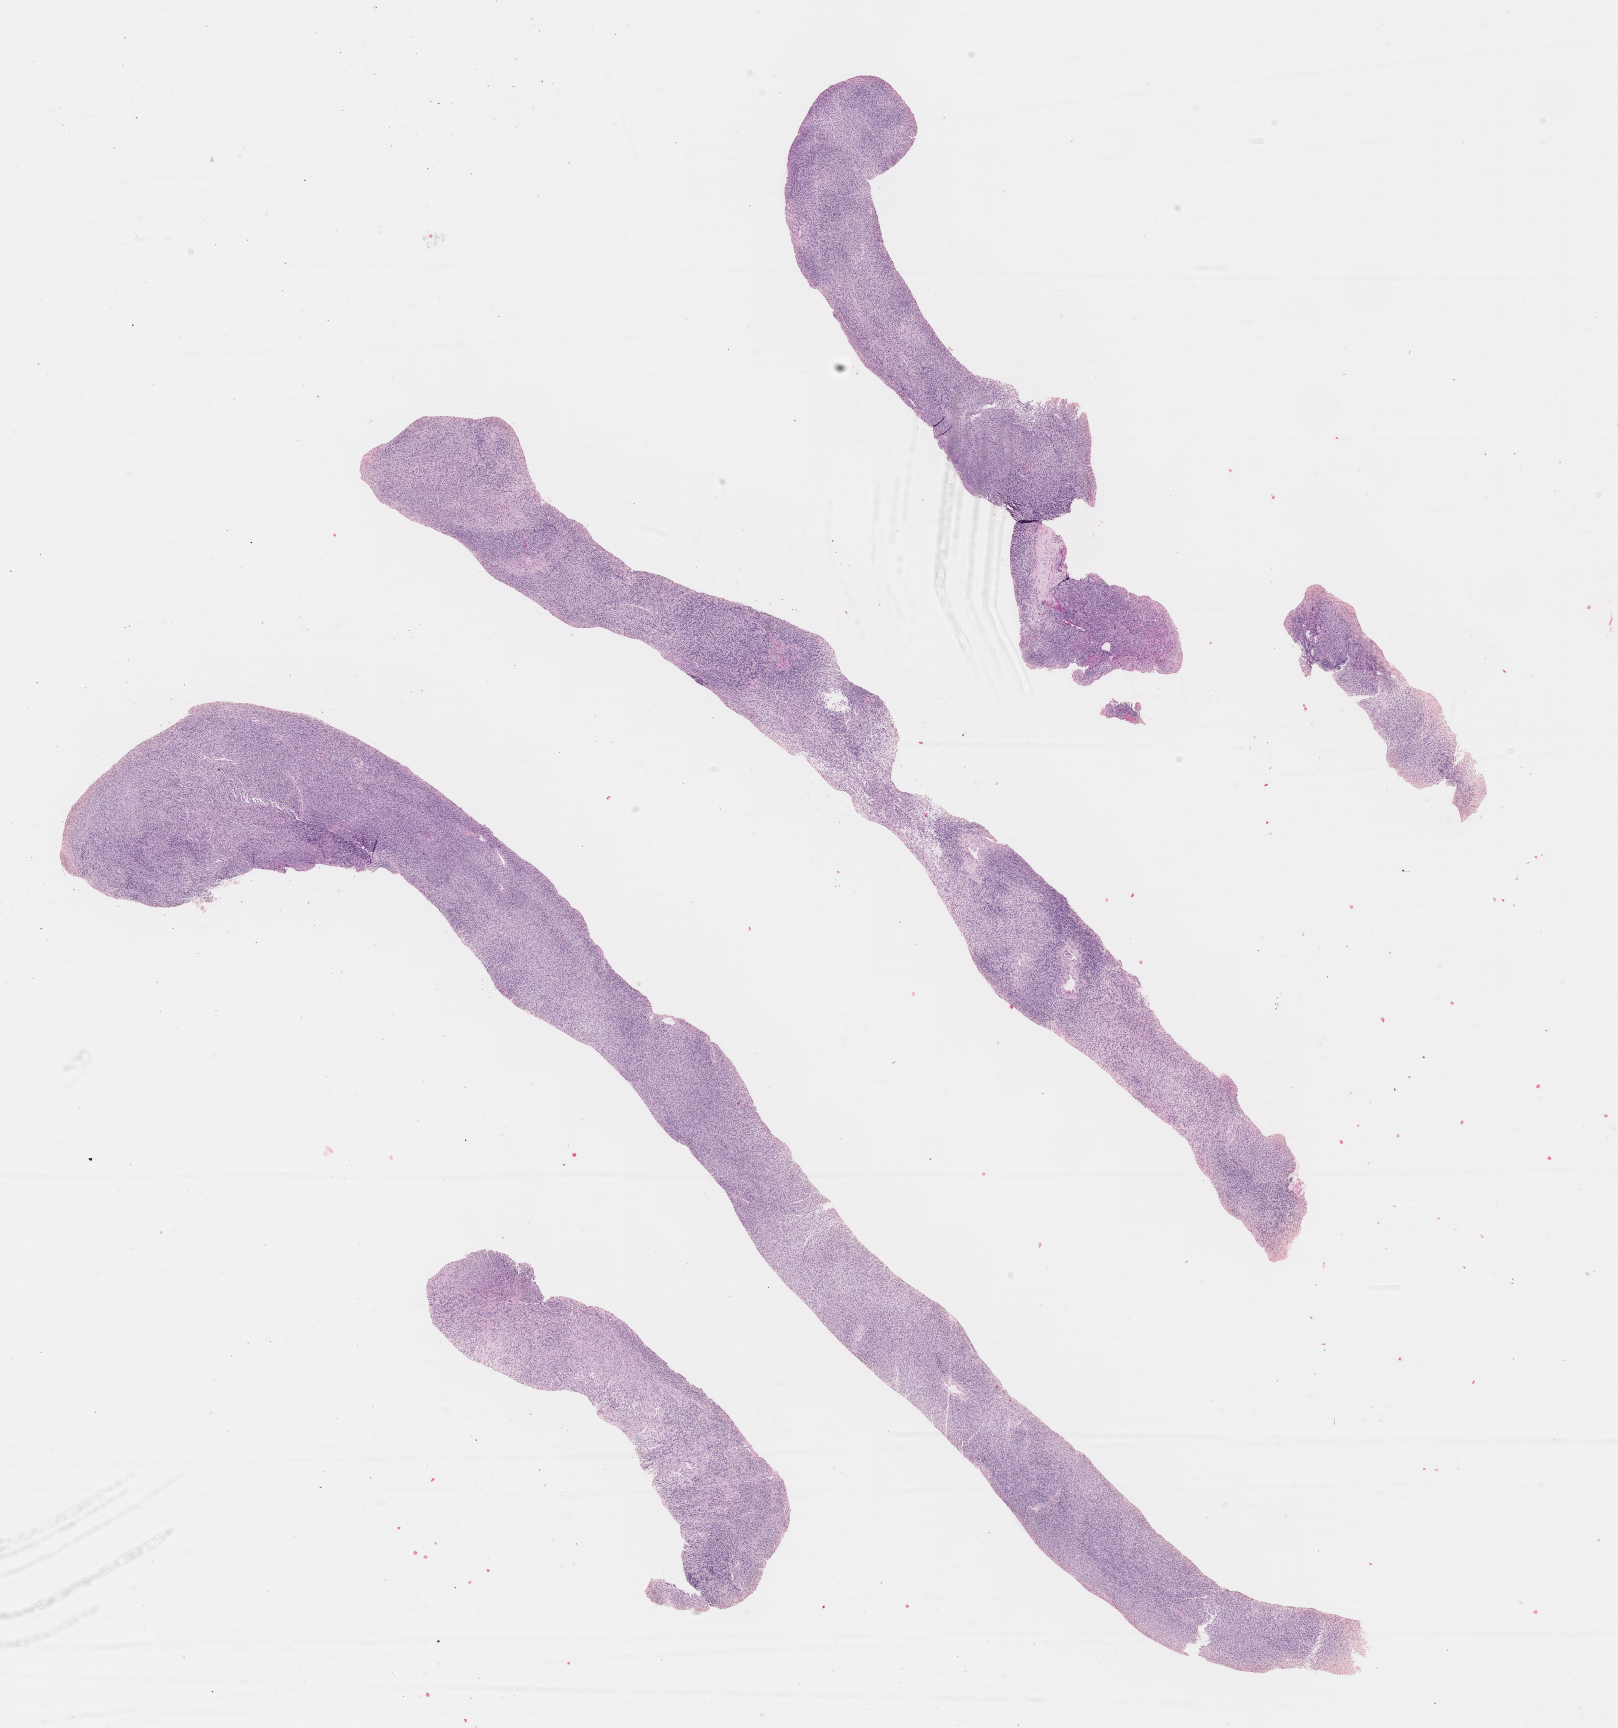
Whole-slide image, hematoxylin and eosin (H&E) stain of tumor tissue — shown as a low-resolution overview of the whole scanned area (about 13.1 x 14.0 mm). FFPE section. Site: pelvis. Male patient, age at diagnosis 0.6 years.
Stage (as recorded): 2. Diagnosis: rhabdomyosarcoma; histological classification: embryonal rhabdomyosarcoma. Metastatic status at presentation (as recorded): non-metastatic (confirmed).